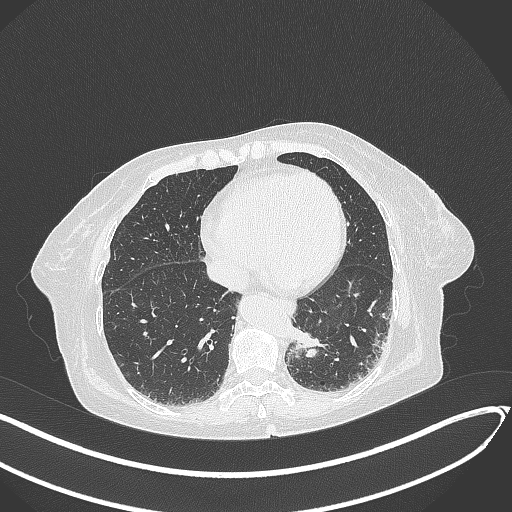
Chest CT, one axial slice; position 65 of 324 along the scan axis; 120 kVp; lung window (W 1500 / L -600 HU); 1 mm slice thickness; 512 × 512 image matrix, field of view 400 × 400 mm. Patient: female, 82 years. Case-level facts recorded for this patient, not image findings: clinical TNM (as recorded): T1b N0 M1.
Annotated regions visible in this slice (rectangle marked by the reading radiologist):
- lung tumour (recorded histology: adenocarcinoma): bounding box [x1, y1, x2, y2] px = [289, 321, 325, 361]